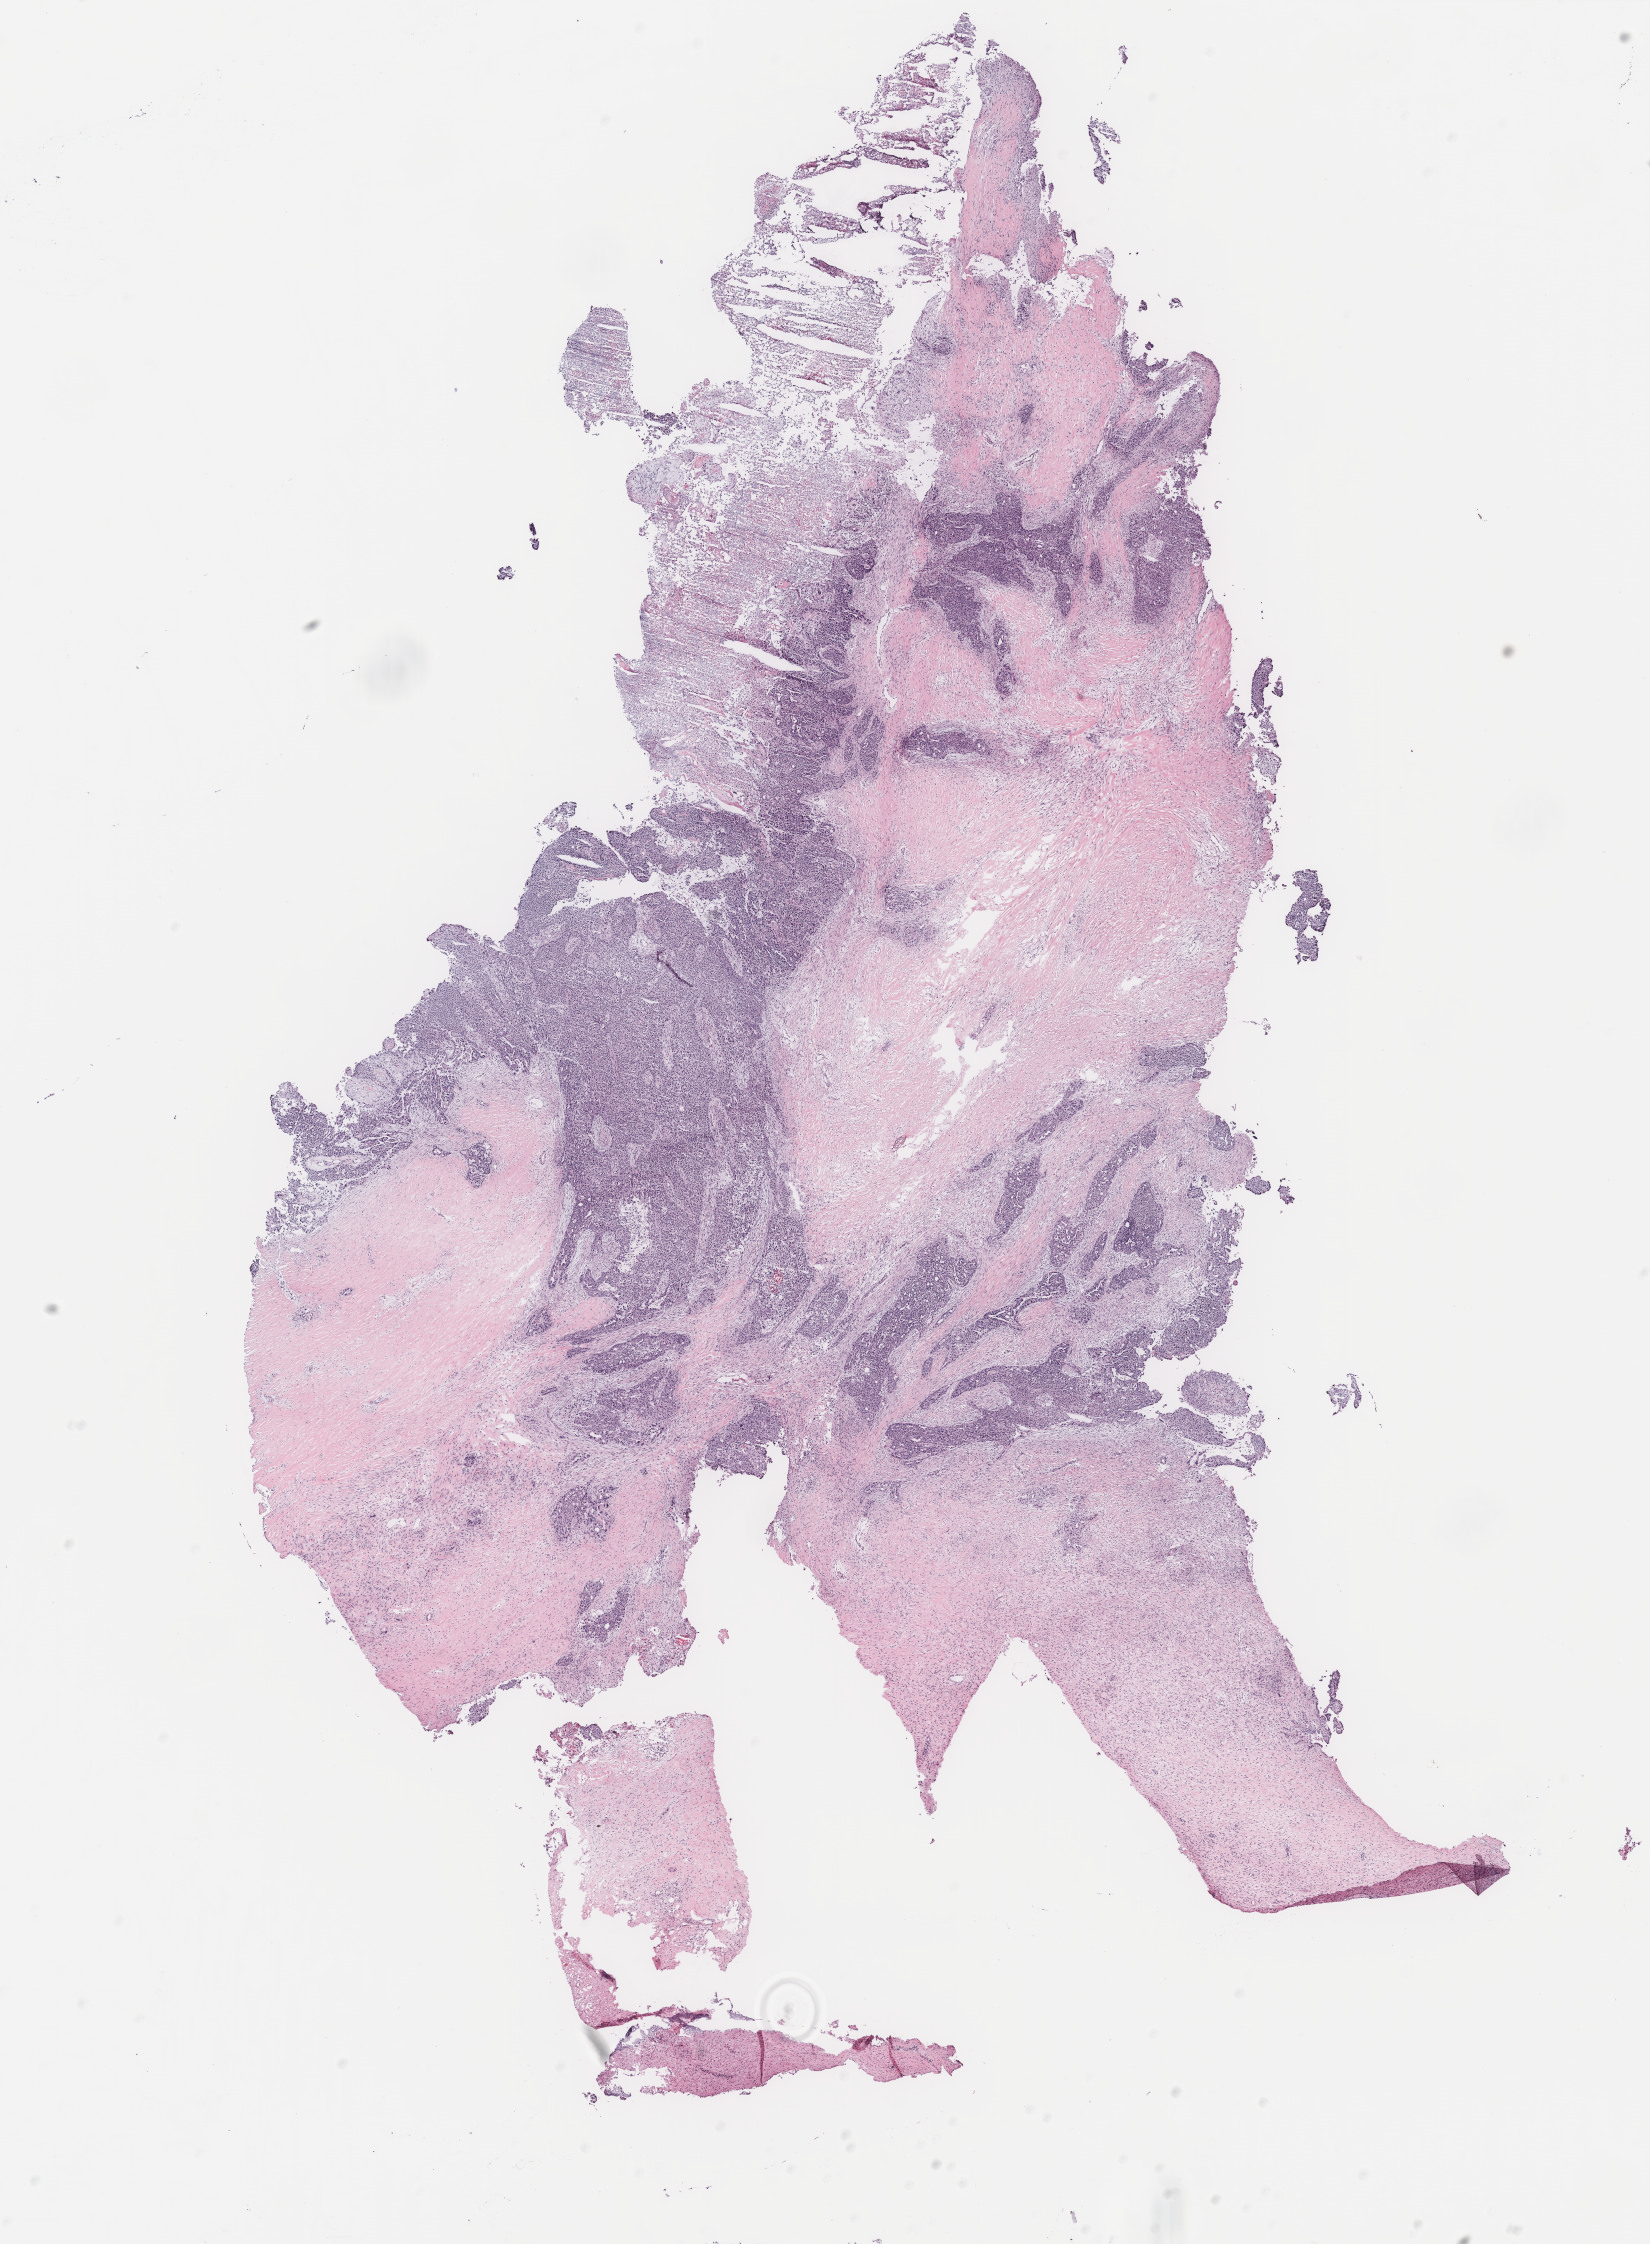
Digitized H&E-stained tissue section (whole slide) — a low-resolution overview of the entire scanned area, about 13.2 x 18.0 mm (from a 40x scan). Tumour tissue sample, ovary. 57-year-old female patient.
Primary tumour site (as recorded): ovary. Histologic diagnosis: Serous adenocarcinoma, NOS.